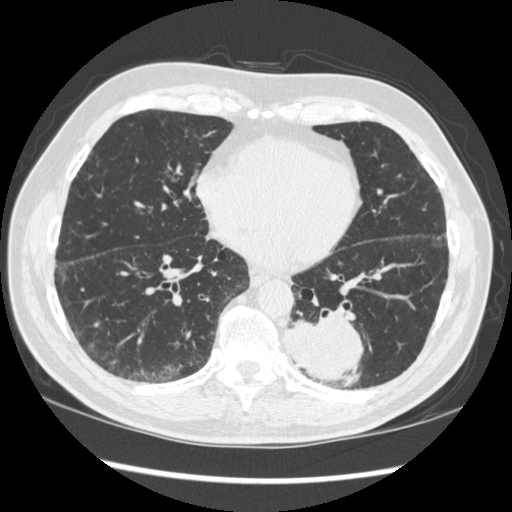
Low-dose screening chest CT, one axial slice; reconstruction kernel STANDARD; 120 kVp; lung window (W 1500 / L -600 HU); 1.25 mm slice thickness; 512 × 512 image matrix, field of view 360 × 360 mm.
Outlined on this slice (expert manual segmentation):
- lesion 1 (tumor, lower lobe of left lung): bounding box [x1, y1, x2, y2] px = [286, 314, 364, 387]